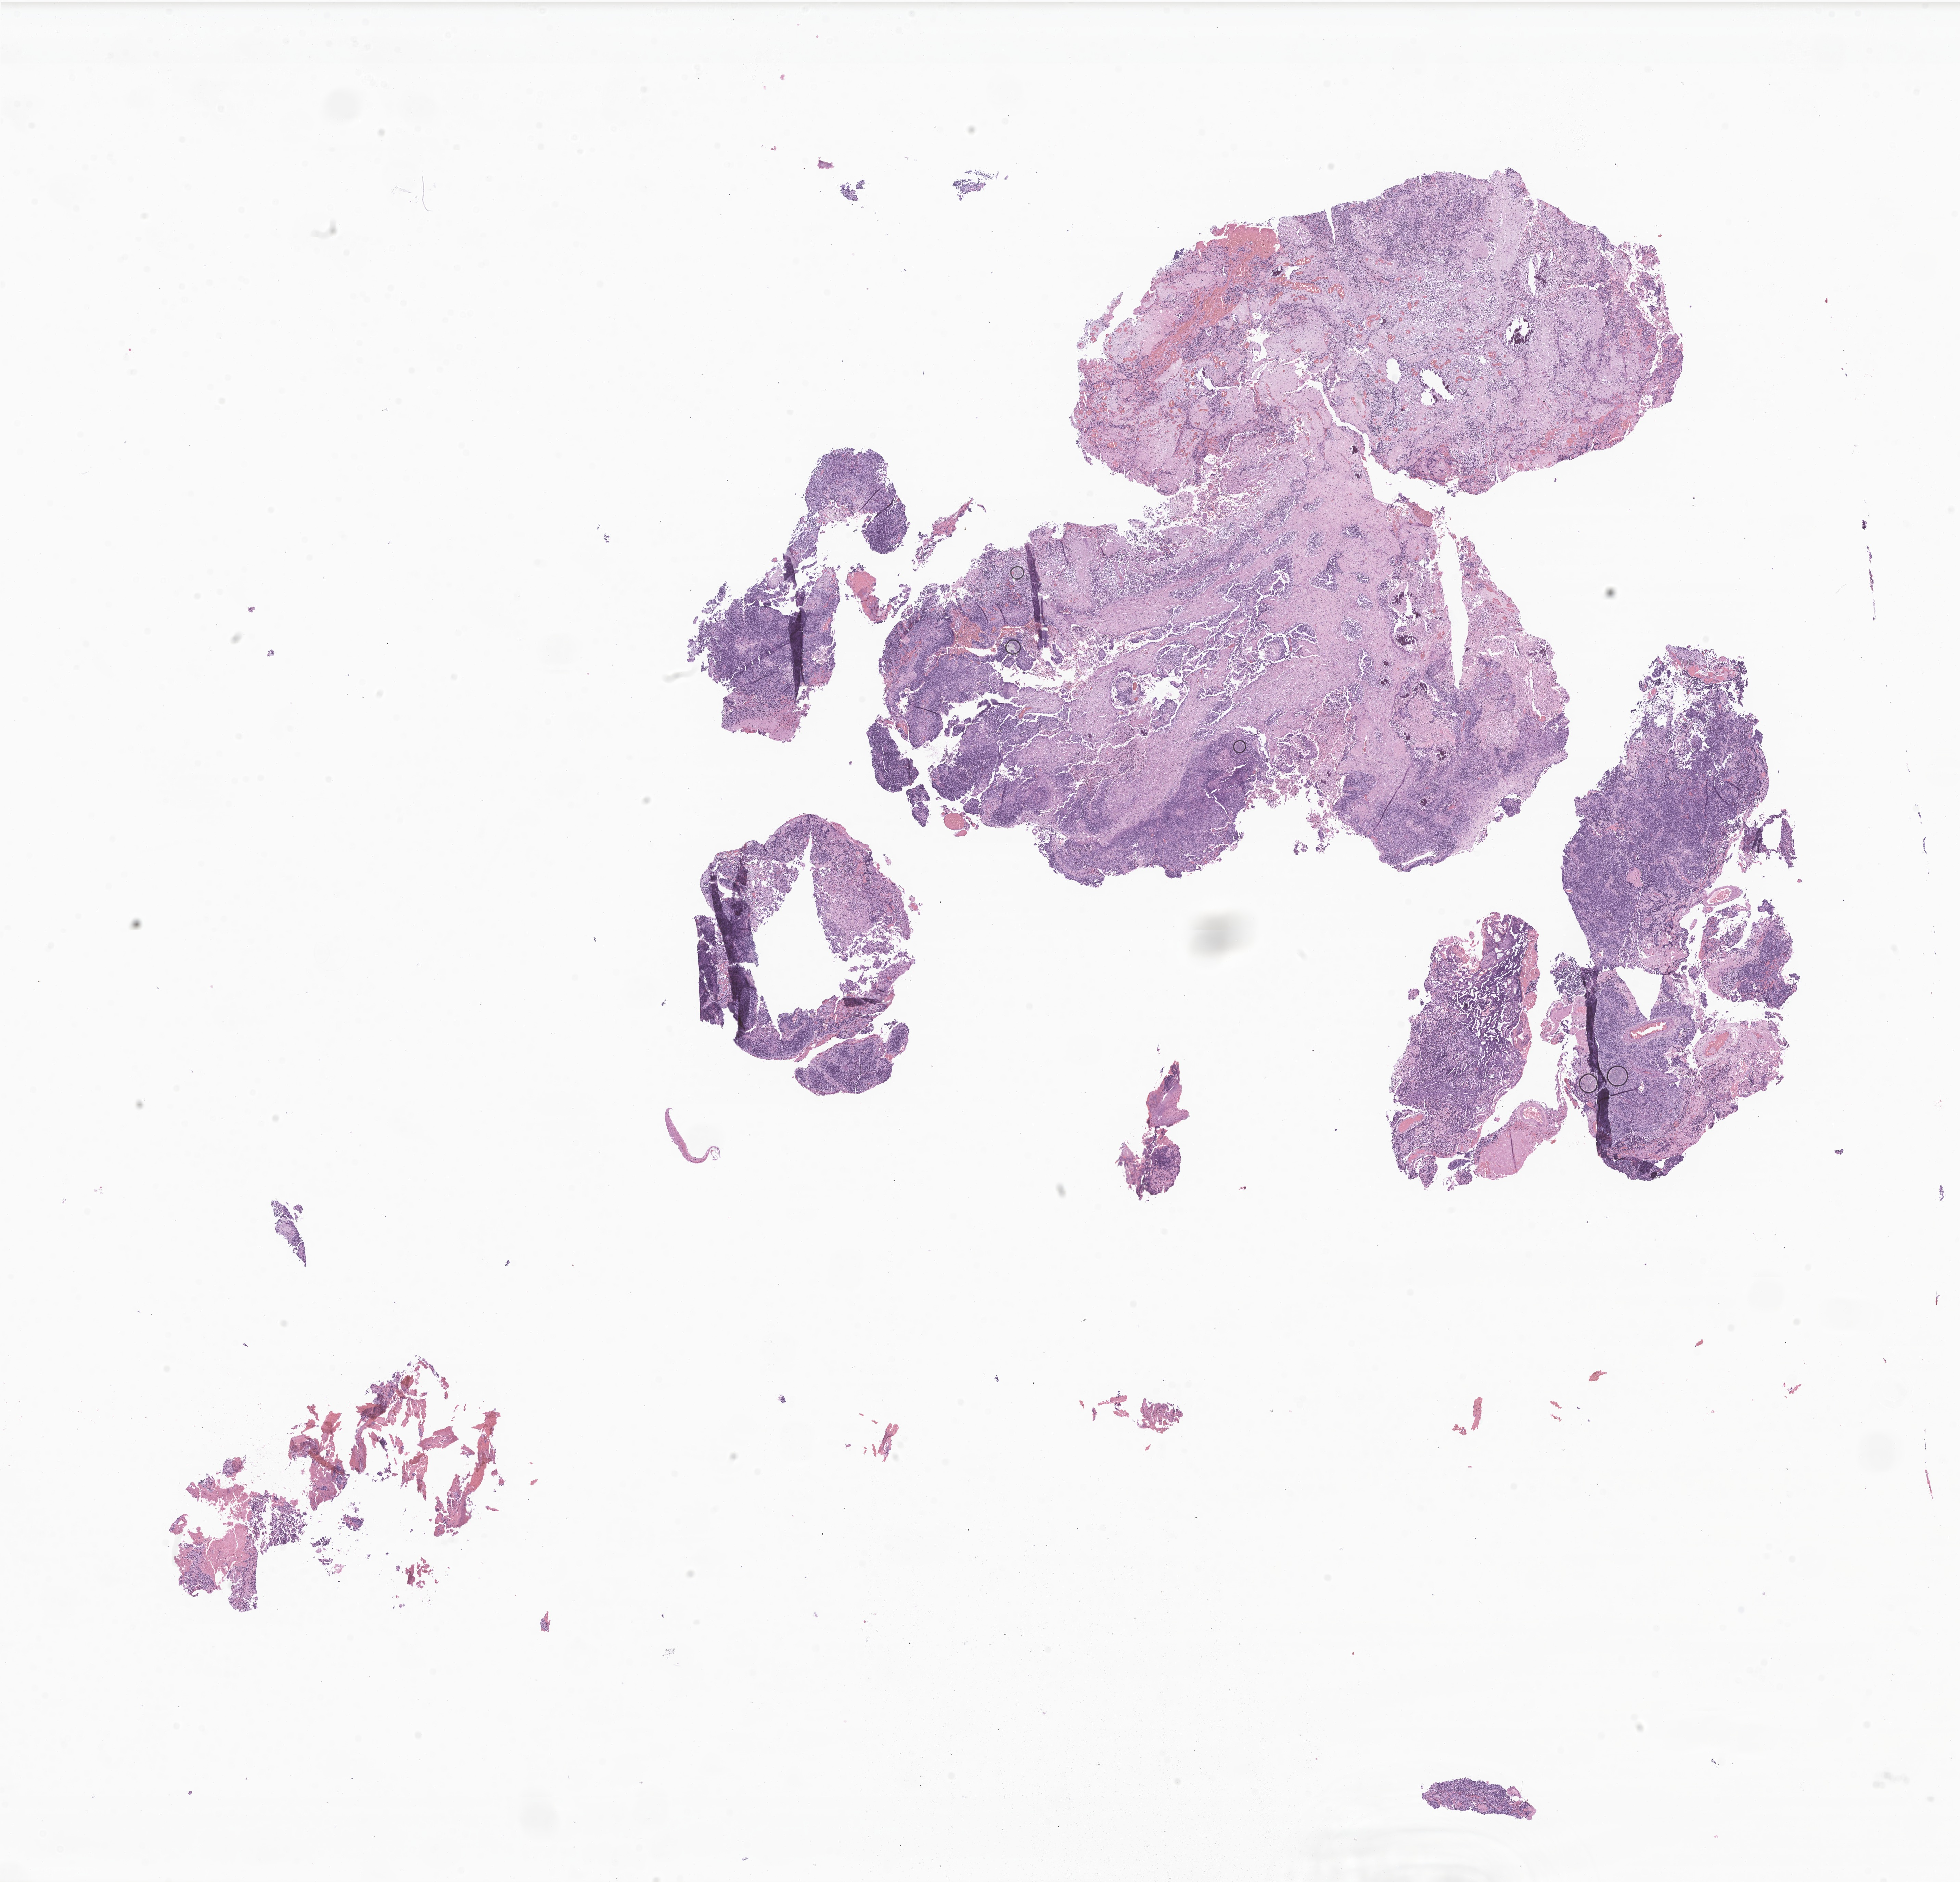
Digitized H&E-stained section of tumor tissue from the brain — shown as a low-resolution overview of the whole scanned area (about 24.1 x 23.2 mm), FFPE section. Patient female; age 551 days (about 1.5 years).
• diagnosis (ICD-O-3 morphology term): Glioma, malignant